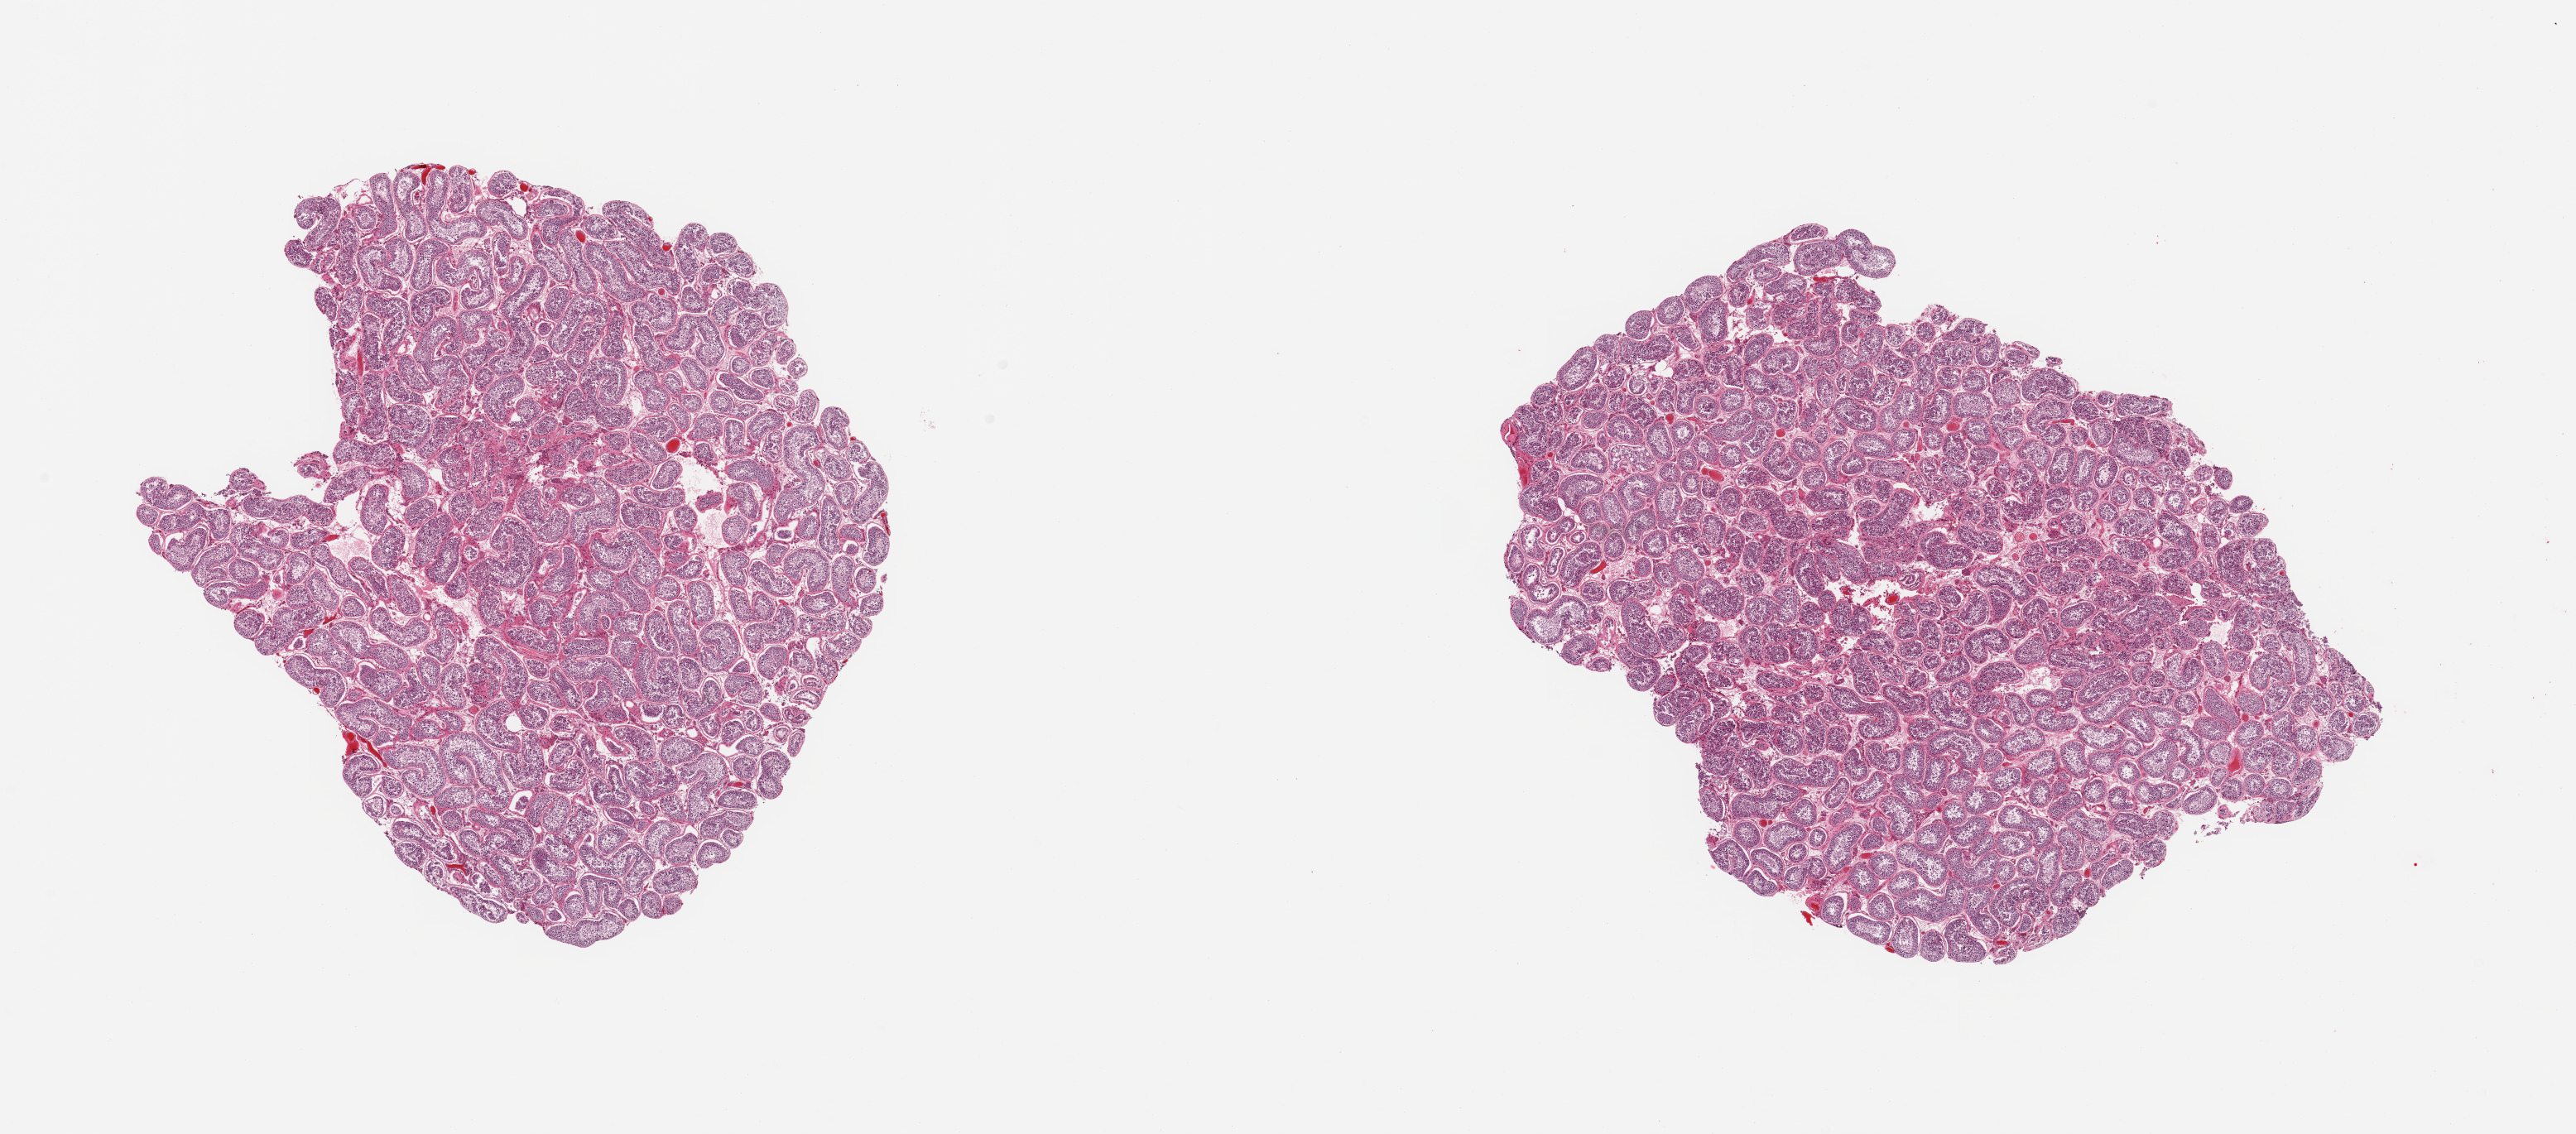
Digitized haematoxylin and eosin-stained section — a low-resolution overview of the entire scanned area, about 24.6 x 10.8 mm, PAXgene-fixed paraffin-embedded (PFPE) section, section of testis (target tissue), donor tissue sample. Donor: male.
Pathologist's review note for this sample: 2 pieces; active spermatogenesis.